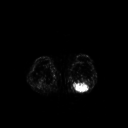
FDG PET of an extremity soft-tissue mass (from a PET/CT study), one axial slice; slice 179 of 267 in the series (ordered by position); 3.27 mm slice thickness; 128 × 128 image matrix, field of view 500 × 500 mm. Patient: male, 54 years. From the clinical record (not read from this slice): histological type: synovial sarcoma; site of the primary tumour: left poplietal fossa.
Annotated regions visible in this slice (expert contour drawn on MRI and transferred to this co-registered scan by the dataset authors):
- gross tumour volume (mass): bounding box (x1, y1, x2, y2) in pixels: (73, 82, 90, 92)